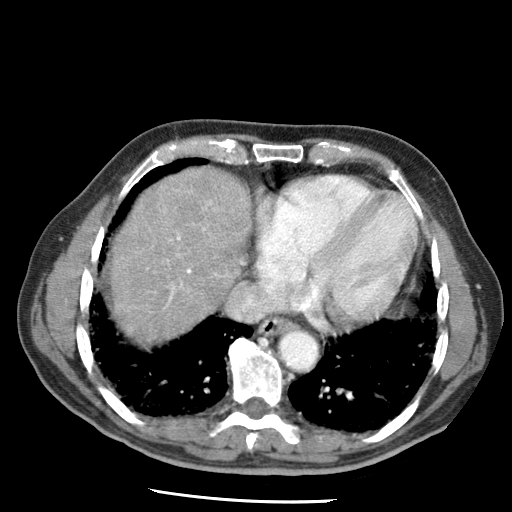
Contrast-enhanced abdominal CT (liver protocol), one axial slice; position 61 of 79 along the scan axis; reconstruction kernel STANDARD; 120 kVp; soft-tissue window (W 400 / L 40 HU); 2.5 mm slice thickness; 512 × 512 image matrix, field of view 320 × 320 mm. Case-level facts recorded for this patient, not image findings: diagnosis: hepatocellular carcinoma (patient treated with transarterial chemoembolisation; whether this scan precedes or follows treatment is not stated here); TNM stage (as recorded): Stage-IIIA; Child-Pugh class: A; tumour size: 7 cm.
Structures marked on this image (semi-automatic segmentation, software-assisted and operator-edited):
- liver parenchyma outside the tumour (the mass and vessels are separate outlines, so this box may not span the whole liver): bounding box <110,168,250,342> (left, top, right, bottom; pixels)
- liver vessels: <167,201,243,302>